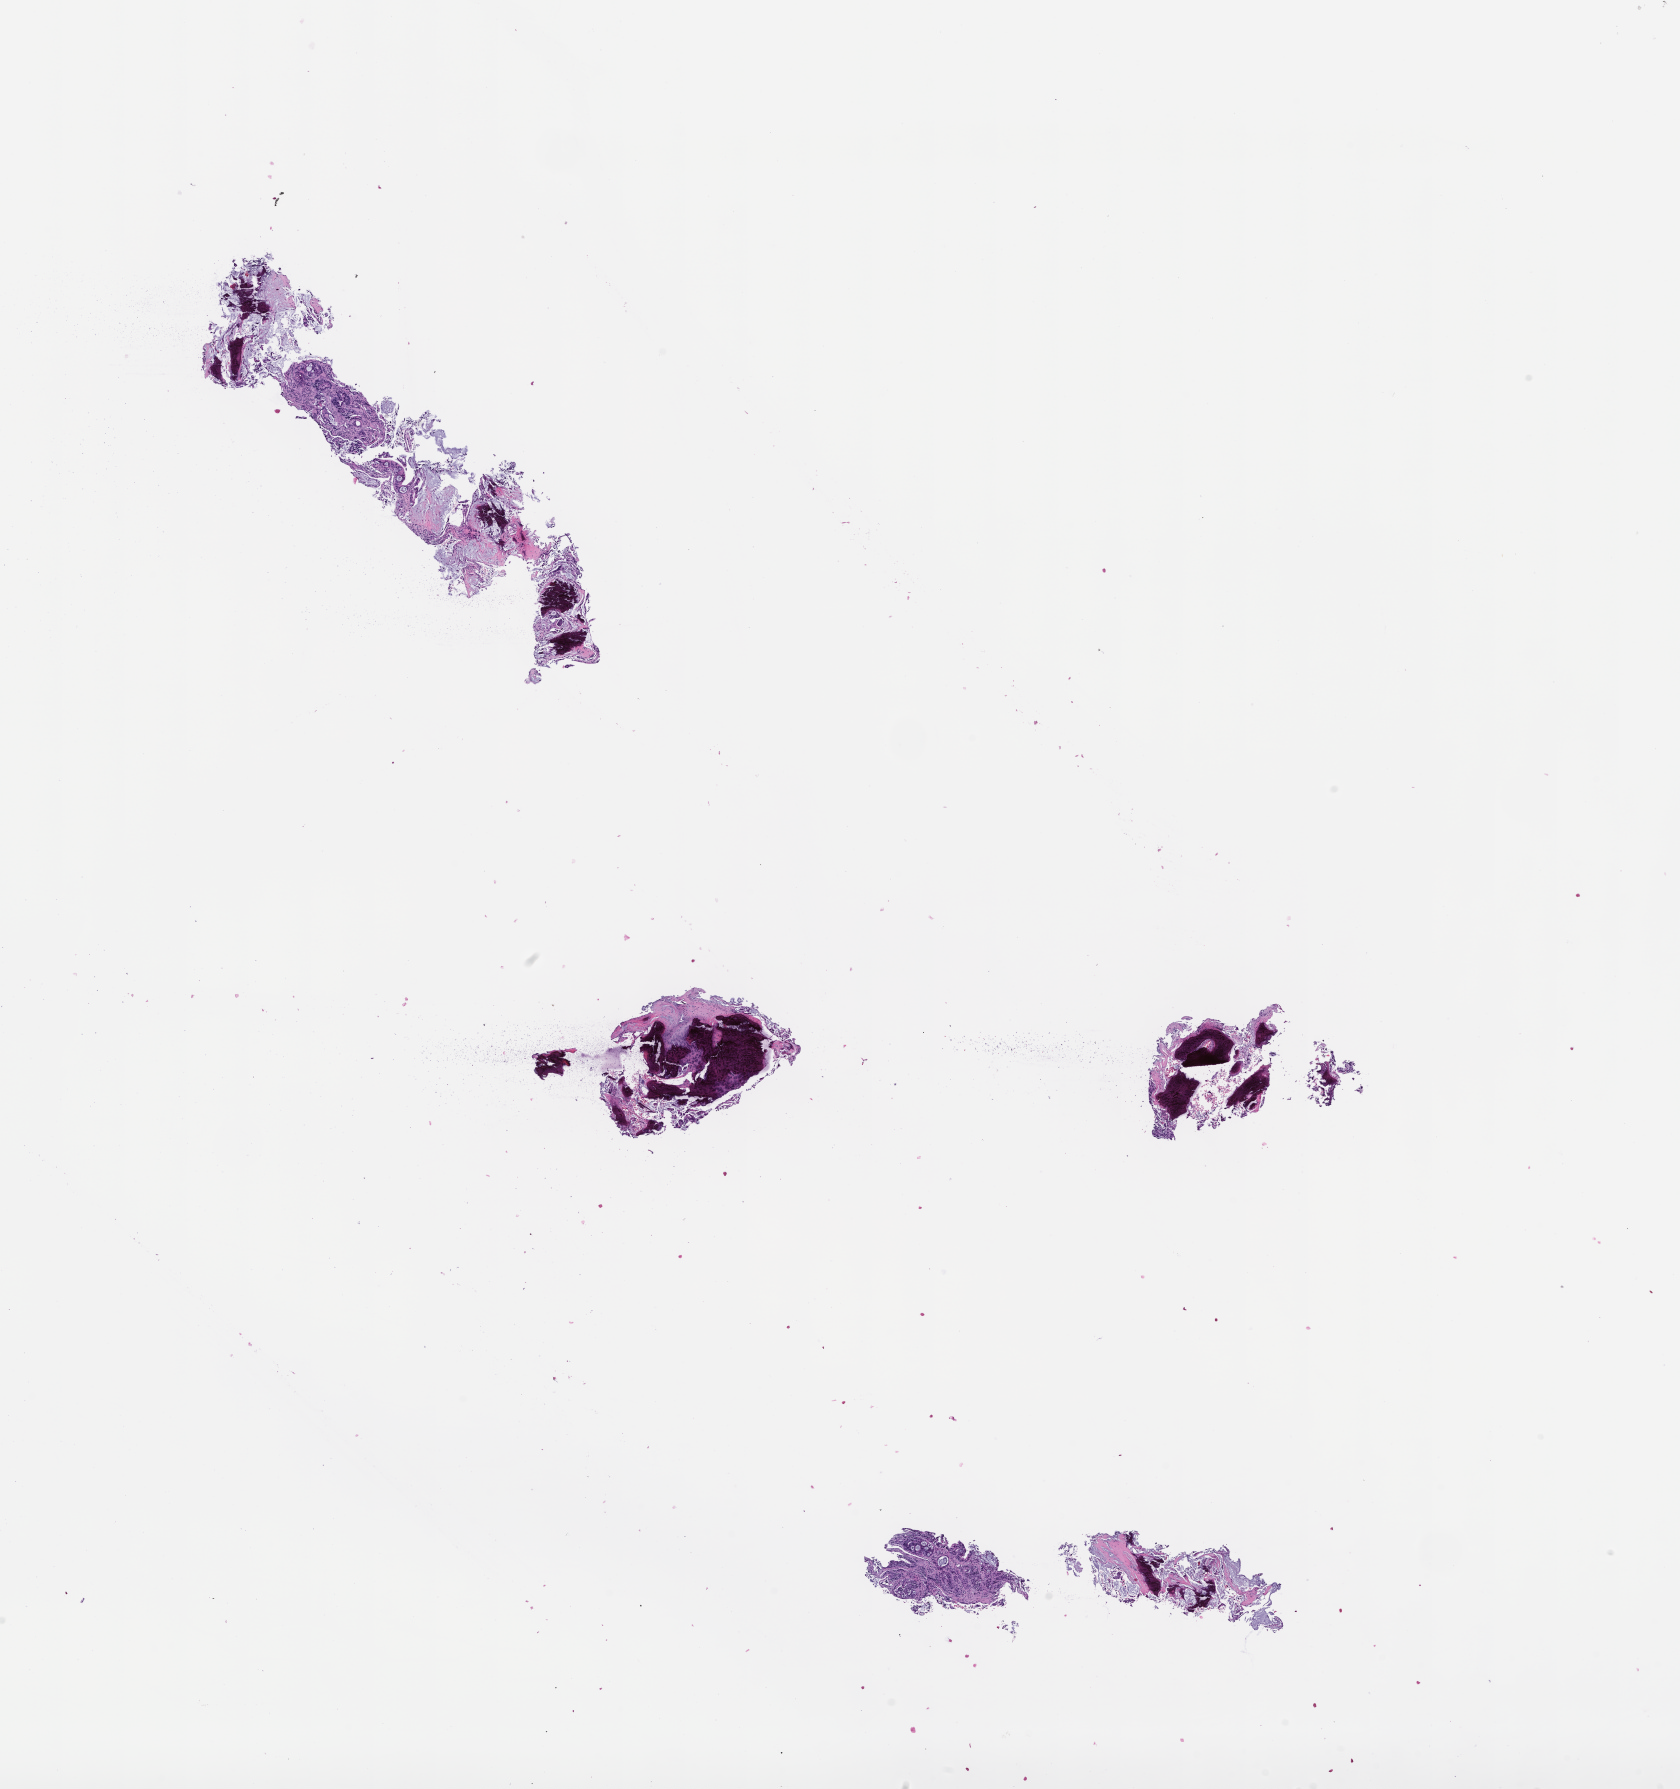
Whole-slide image, haematoxylin and eosin stain — a low-resolution overview of the entire scanned area, about 13.6 x 14.5 mm. Formalin-fixed, paraffin-embedded (FFPE) tissue. Patient sex: female.
This section: metastatic tumor tissue. Patient diagnosis (primary): Colorectal Carcinoma.